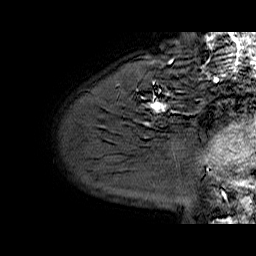
Breast MRI (dynamic contrast-enhanced), one sagittal slice; slice 50 of 60 in the series (ordered by position); dynamic contrast-enhanced series, time point 2 of 6 at this slice position (early post-contrast); 1.5 T; TE 6.4 ms, TR 32.9 ms; 256 × 256 image matrix. Female patient. From the clinical record (not read from this slice): setting: breast cancer imaged before/during neoadjuvant chemotherapy; receptor status: HER2-positive.
Outlined on this slice (semi-automatic segmentation, software-assisted and operator-edited):
- analysis volume of interest (the breast-tissue region the enhancement analysis was run in; not a lesion): bounding box <130,62,205,128> (left, top, right, bottom; pixels)
- tumour enhancement mask (voxels above the 100 % enhancement threshold inside the analysis volume of interest): <151,62,170,112>